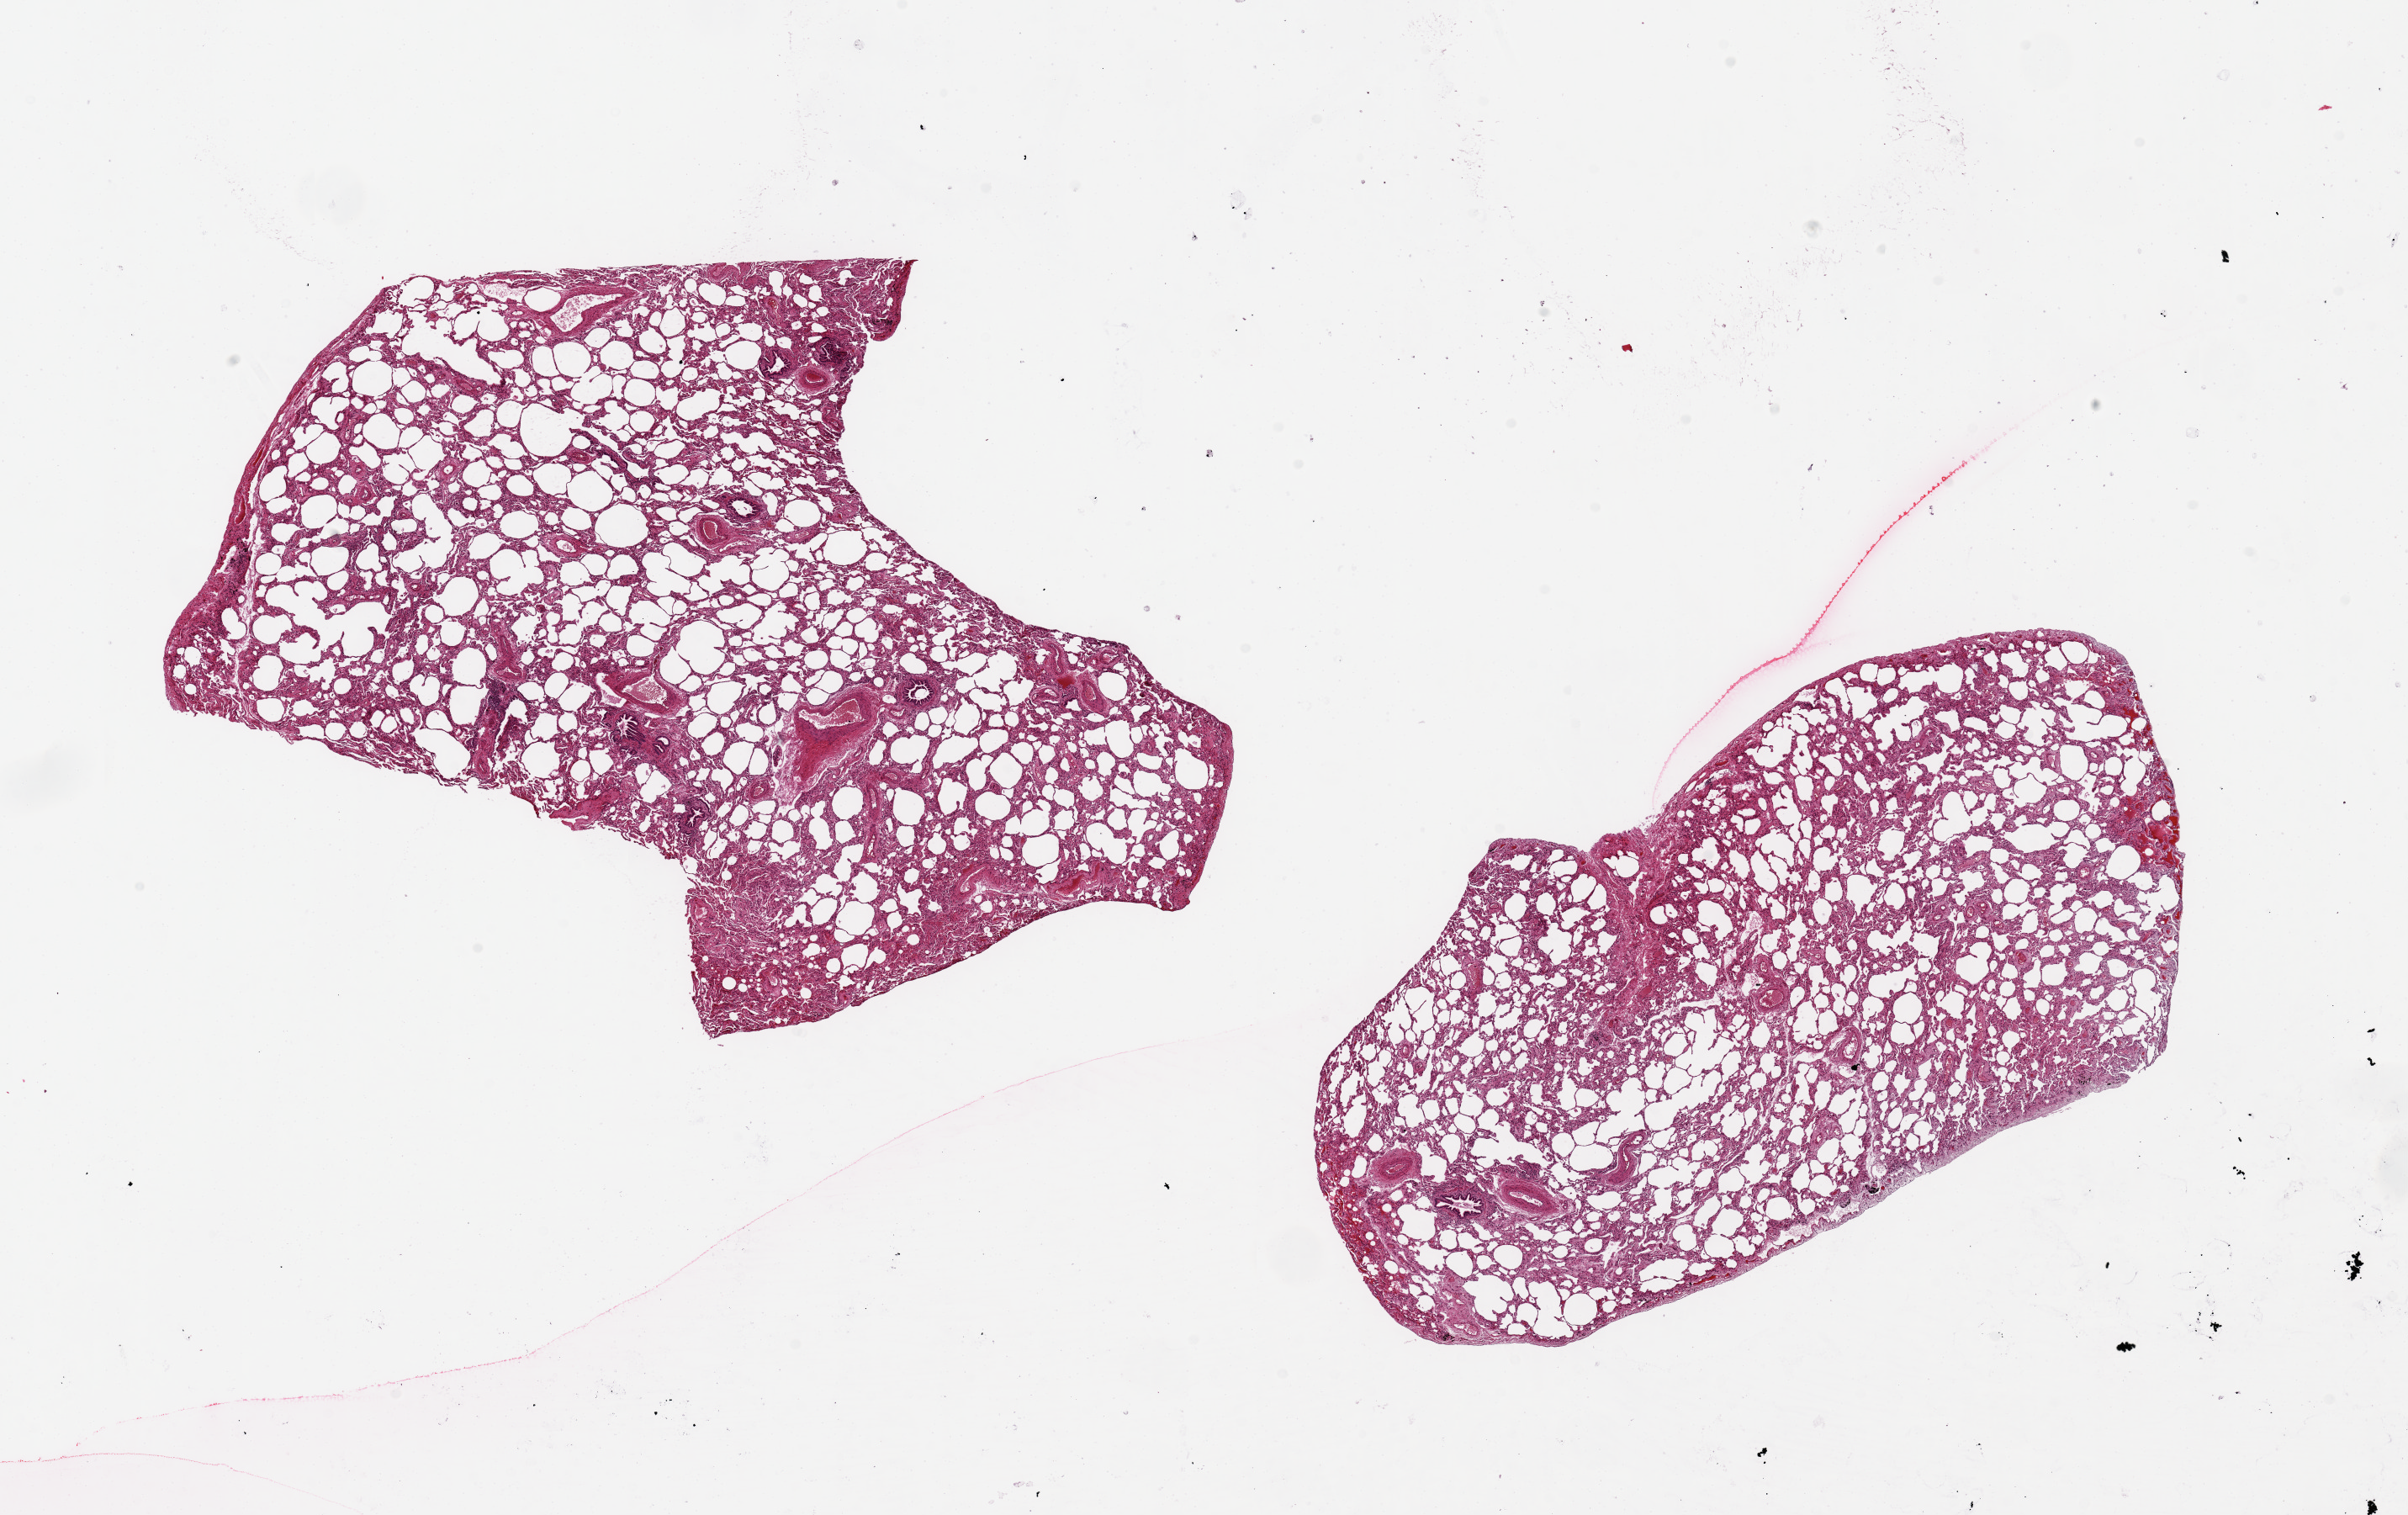
Hematoxylin and eosin (H&E) whole-slide image — whole scanned area (about 22.6 x 14.2 mm, from a 20x scan) shown as a low-resolution overview; PAXgene-fixed paraffin-embedded (PFPE) section; target tissue: lung; donor tissue sample. Donor sex: female.
Pathologist's review note for this sample: 2 pieces: 9x7 & 8x5 mm; panacinar emphysema, no fibrosis or inflammation.